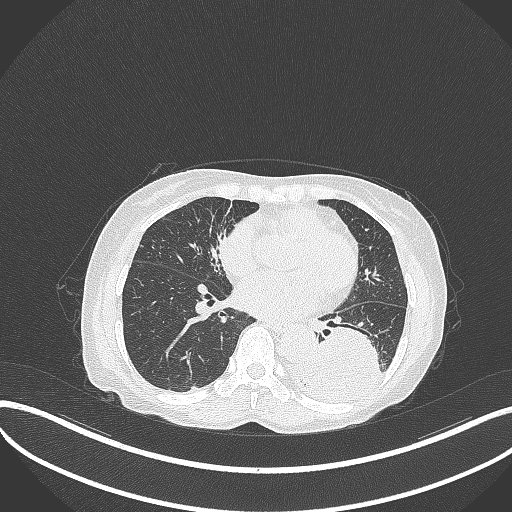
Chest CT, one axial slice; slice 131 of 370 in the series (ordered by position); reconstruction kernel B70f; lung window (W 1500 / L -600 HU); 1 mm slice thickness; 512 × 512 image matrix. Female patient, age 78 years. Case-level facts recorded for this patient, not image findings: clinical TNM (as recorded): T3 N0 M1.
Structures marked on this image (bounding box drawn by a radiologist):
- lung tumour (recorded histology: squamous cell carcinoma): box from (x=305, y=322) to (x=394, y=401) px